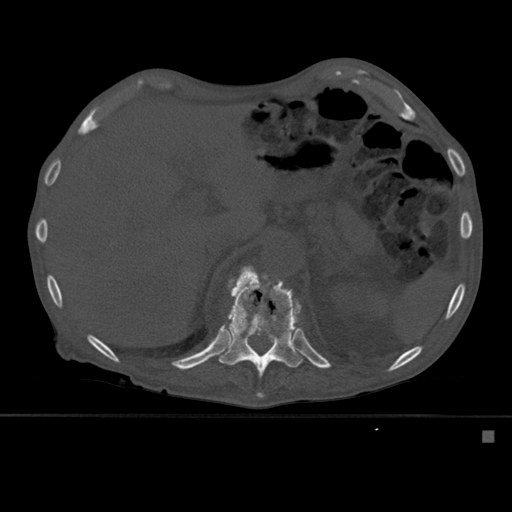
CT including the spine, one axial slice; slice 278 of 527 in the series (ordered by position); bone window (W 1800 / L 400 HU); 1.5 mm slice thickness; 512 × 512 image matrix. Patient: male, 78 years. From the clinical record (not read from this slice): primary cancer: prostate.
Annotated regions visible in this slice (semi-automatic segmentation, software-assisted and operator-edited):
- T11 vertebra: box from (x=221, y=265) to (x=290, y=366) px
- T12 vertebra: (x=218, y=268)–(x=303, y=398)
- T9 vertebra: (x=225, y=344)–(x=231, y=360)